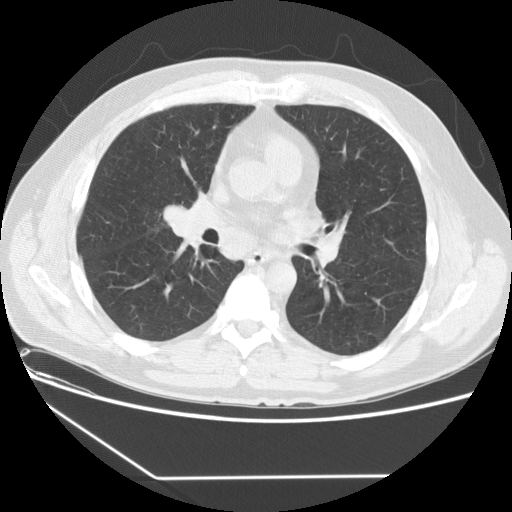
Low-dose screening chest CT, one axial slice. Position 81 of 154 along the scan axis. Reconstruction kernel STANDARD. 120 kVp. Lung window (W 1500 / L -600 HU). 2.5 mm slice thickness. 512 × 512 image matrix, field of view 370 × 370 mm.
Annotated regions visible in this slice (manually delineated by an expert):
- lesion 1 (tumor, middle lobe of right lung): box from (x=162, y=205) to (x=204, y=244) px